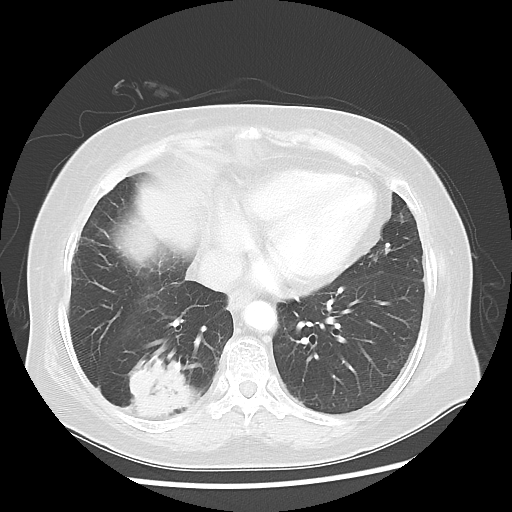
Chest CT, one axial slice; position 19 of 56 along the scan axis; 120 kVp; lung window (W 1500 / L -600 HU); 5 mm slice thickness; 512 × 512 image matrix, field of view 360 × 360 mm. Female patient, age 64 years. Case-level facts recorded for this patient, not image findings: clinical TNM (as recorded): Tis N0 M0.
Outlined on this slice (bounding box drawn by a radiologist):
- lung tumour (recorded histology: adenocarcinoma): bounding box (x1, y1, x2, y2) in pixels: (124, 358, 206, 431)